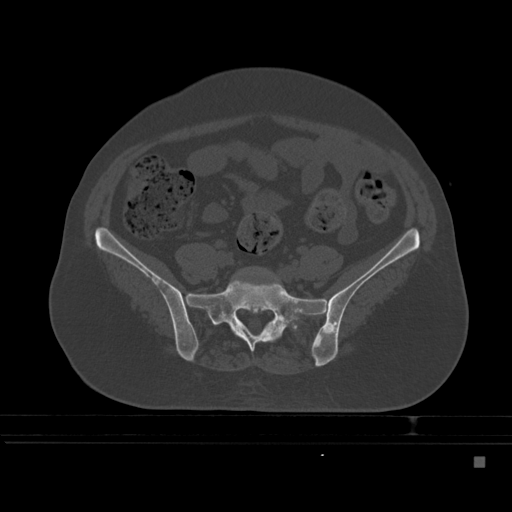
CT including the spine, one axial slice. Slice 95 of 495 in the series (ordered by position). Bone window (W 1800 / L 400 HU). 1.5 mm slice thickness. 512 × 512 image matrix. Female patient, age 33 years. From the clinical record (not read from this slice): primary cancer: breast; vertebrae with lytic lesions (as recorded): T1.
Annotated regions visible in this slice (semi-automatic segmentation, software-assisted and operator-edited):
- L5 vertebra: box from (x=243, y=266) to (x=259, y=271) px